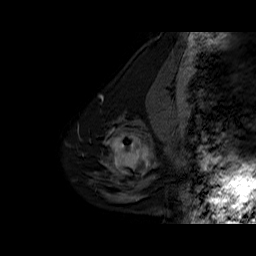
Breast MRI (dynamic contrast-enhanced), one sagittal slice. Slice 16 of 60 in the series (ordered by position). Dynamic contrast-enhanced series, time point 2 of 6 at this slice position (early post-contrast). 1.5 T. TE 6.3 ms, TR 32.5 ms. 4 mm slice thickness. 256 × 256 image matrix, field of view 200 × 200 mm. Female patient. From the clinical record (not read from this slice): setting: breast cancer imaged before/during neoadjuvant chemotherapy; receptor status: triple-negative.
Annotated regions visible in this slice (semi-automatically segmented with operator editing):
- analysis volume of interest (the breast-tissue region the enhancement analysis was run in; not a lesion): bounding box (x1, y1, x2, y2) in pixels: (102, 127, 162, 186)
- tumour enhancement mask (voxels above the 100 % enhancement threshold inside the analysis volume of interest): (105, 133, 152, 174)